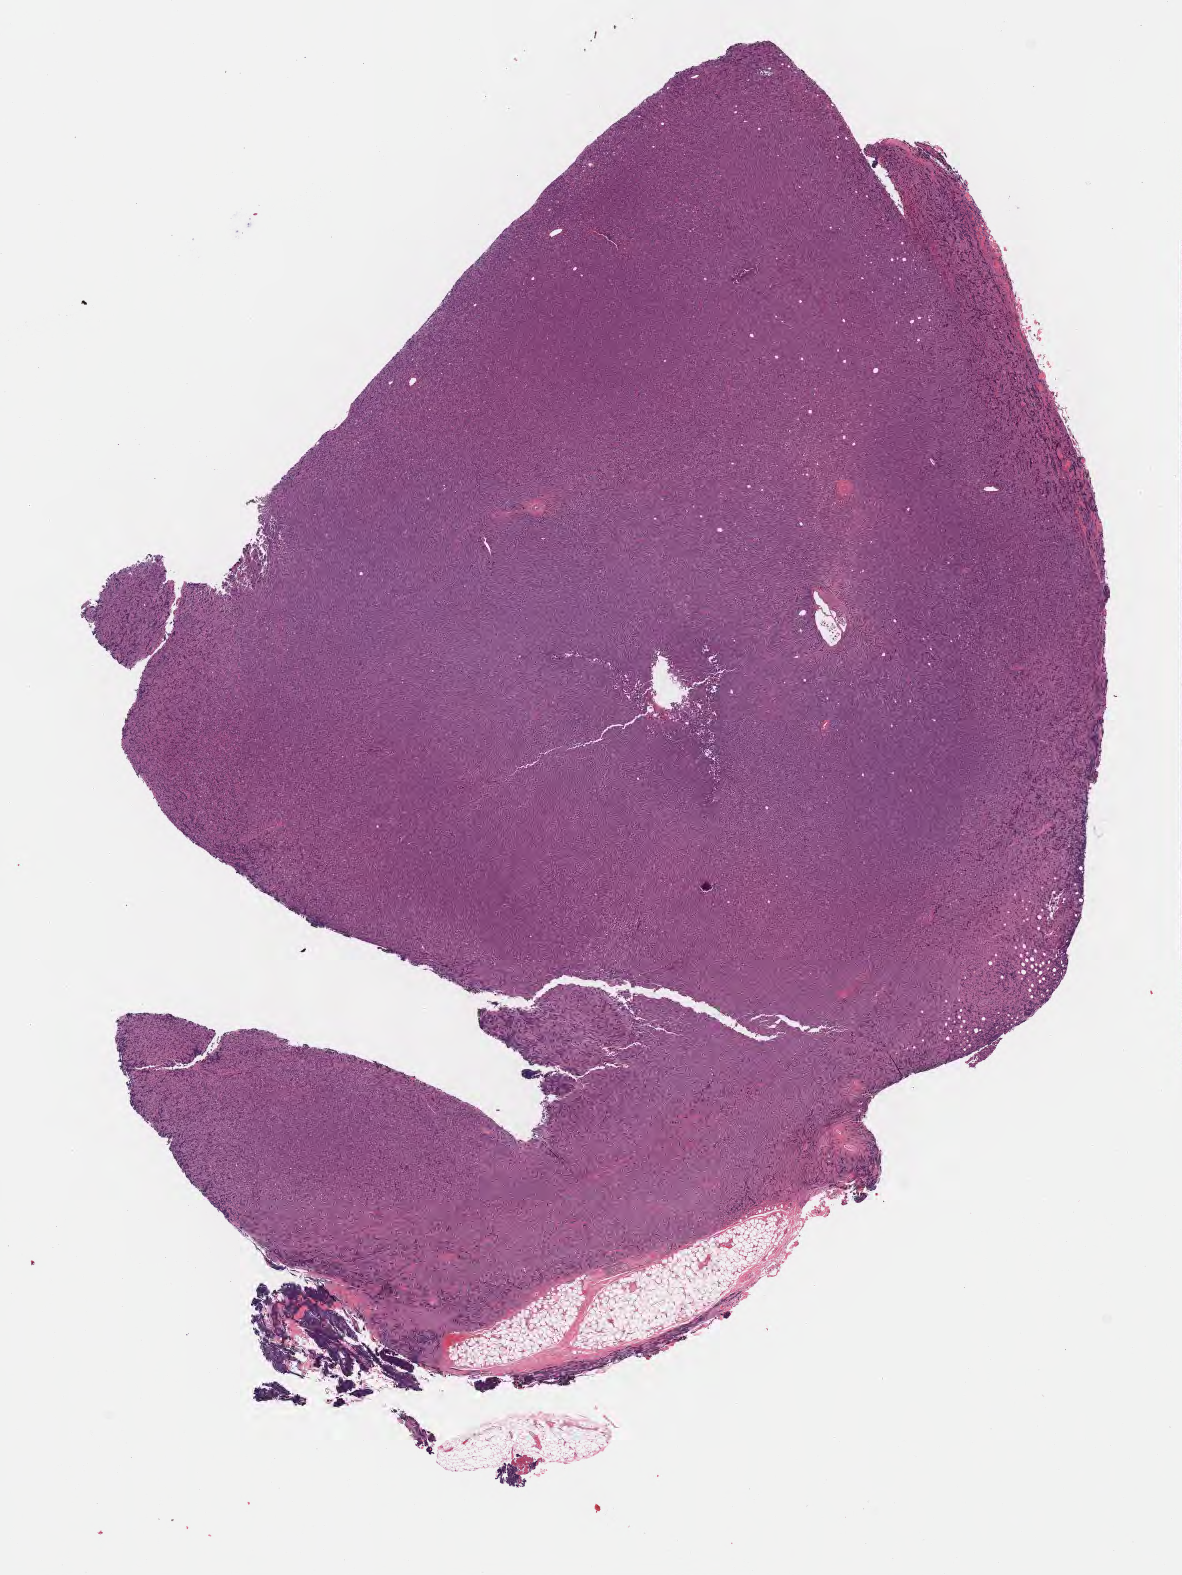
Digitized H&E-stained section — whole scanned area (about 9.6 x 12.7 mm) shown as a low-resolution overview; specimen: tumor tissue; site: lymph node. Patient male; 26 years old.
Diagnosis: Diffuse large B-cell lymphoma, NOS.